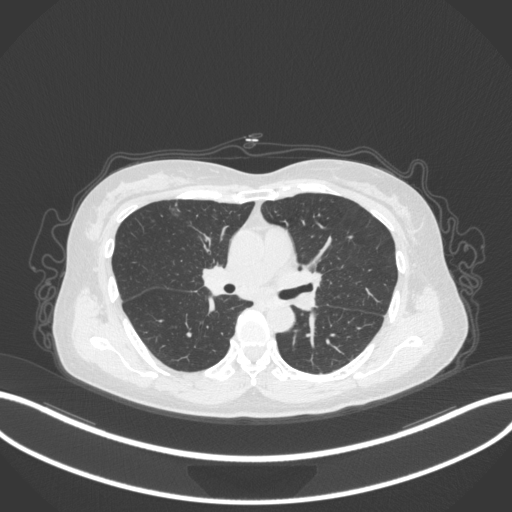
Chest CT, one axial slice; position 192 of 317 along the scan axis; 120 kVp; lung window (W 1500 / L -600 HU); 1 mm slice thickness; 512 × 512 image matrix, field of view 400 × 400 mm. Patient: female, 61 years. From the clinical record (not read from this slice): clinical TNM (as recorded): T1b N0 M0.
Annotated regions visible in this slice (bounding box drawn by a radiologist):
- lung tumour (recorded histology: adenocarcinoma): box from (x=165, y=198) to (x=184, y=218) px